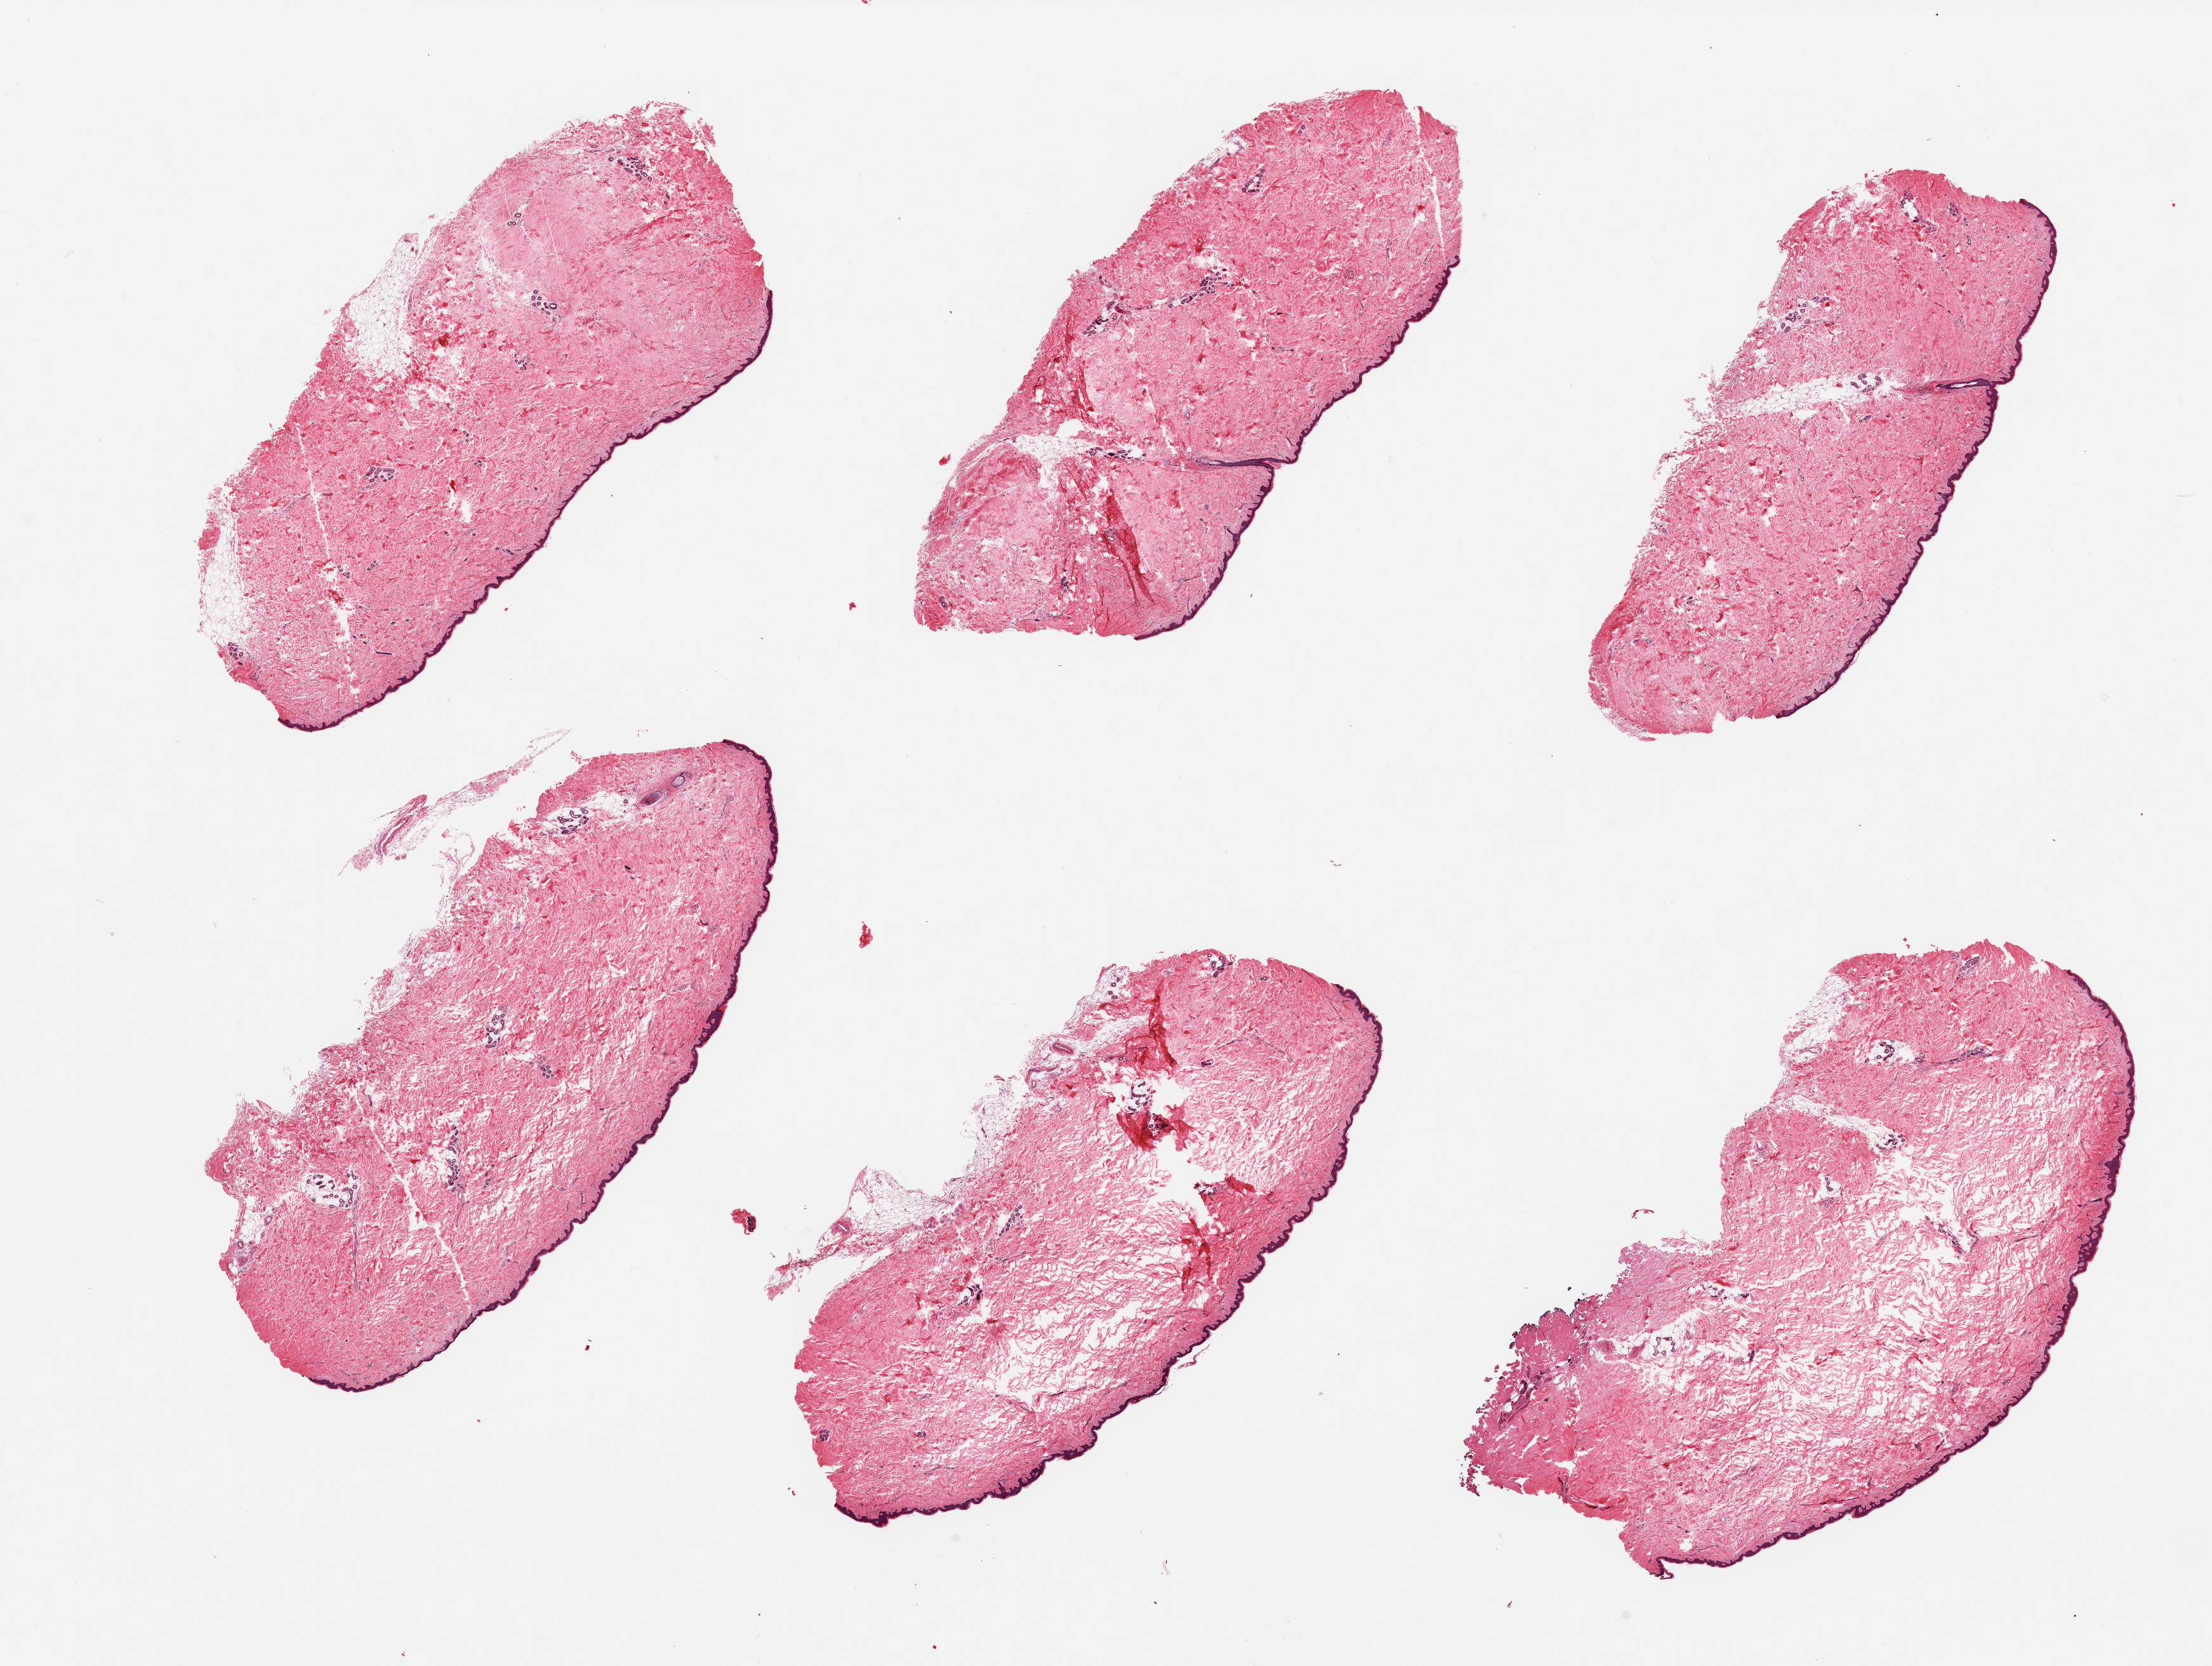
Digitized H&E-stained section — a low-resolution overview of the entire scanned area, about 27.6 x 20.8 mm; PAXgene-fixed, paraffin-embedded tissue; sampled site (target tissue): skin of suprapubic region; tissue donor sample. Donor sex: female.
- reviewer comment on this tissue sample: 6 pieces, each with ~5-10% internal and attached dermal fat